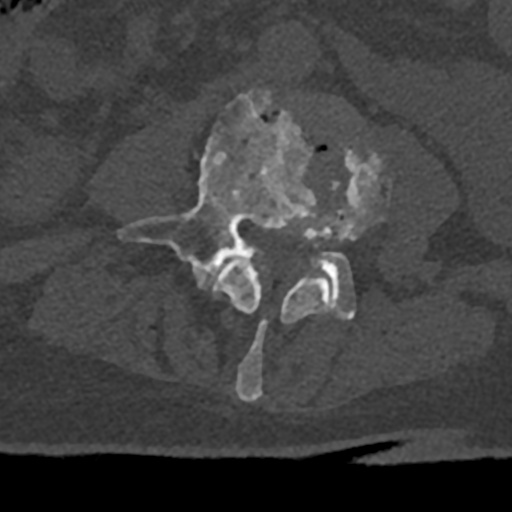
CT including the spine, one axial slice. Slice 284 of 797 in the series (ordered by position). 120 kVp. Bone window (W 1800 / L 400 HU). 0.5 mm slice thickness. 512 × 512 image matrix. Male patient, age 74 years. From the clinical record (not read from this slice): primary cancer: renal; vertebrae with lytic lesions (as recorded): T10, L1, L2, L3, L4, L5.
Annotated regions visible in this slice (semi-automatic segmentation, software-assisted and operator-edited):
- L3 vertebra: box from (x=215, y=143) to (x=384, y=401) px
- L4 vertebra: (x=117, y=90)–(x=354, y=320)